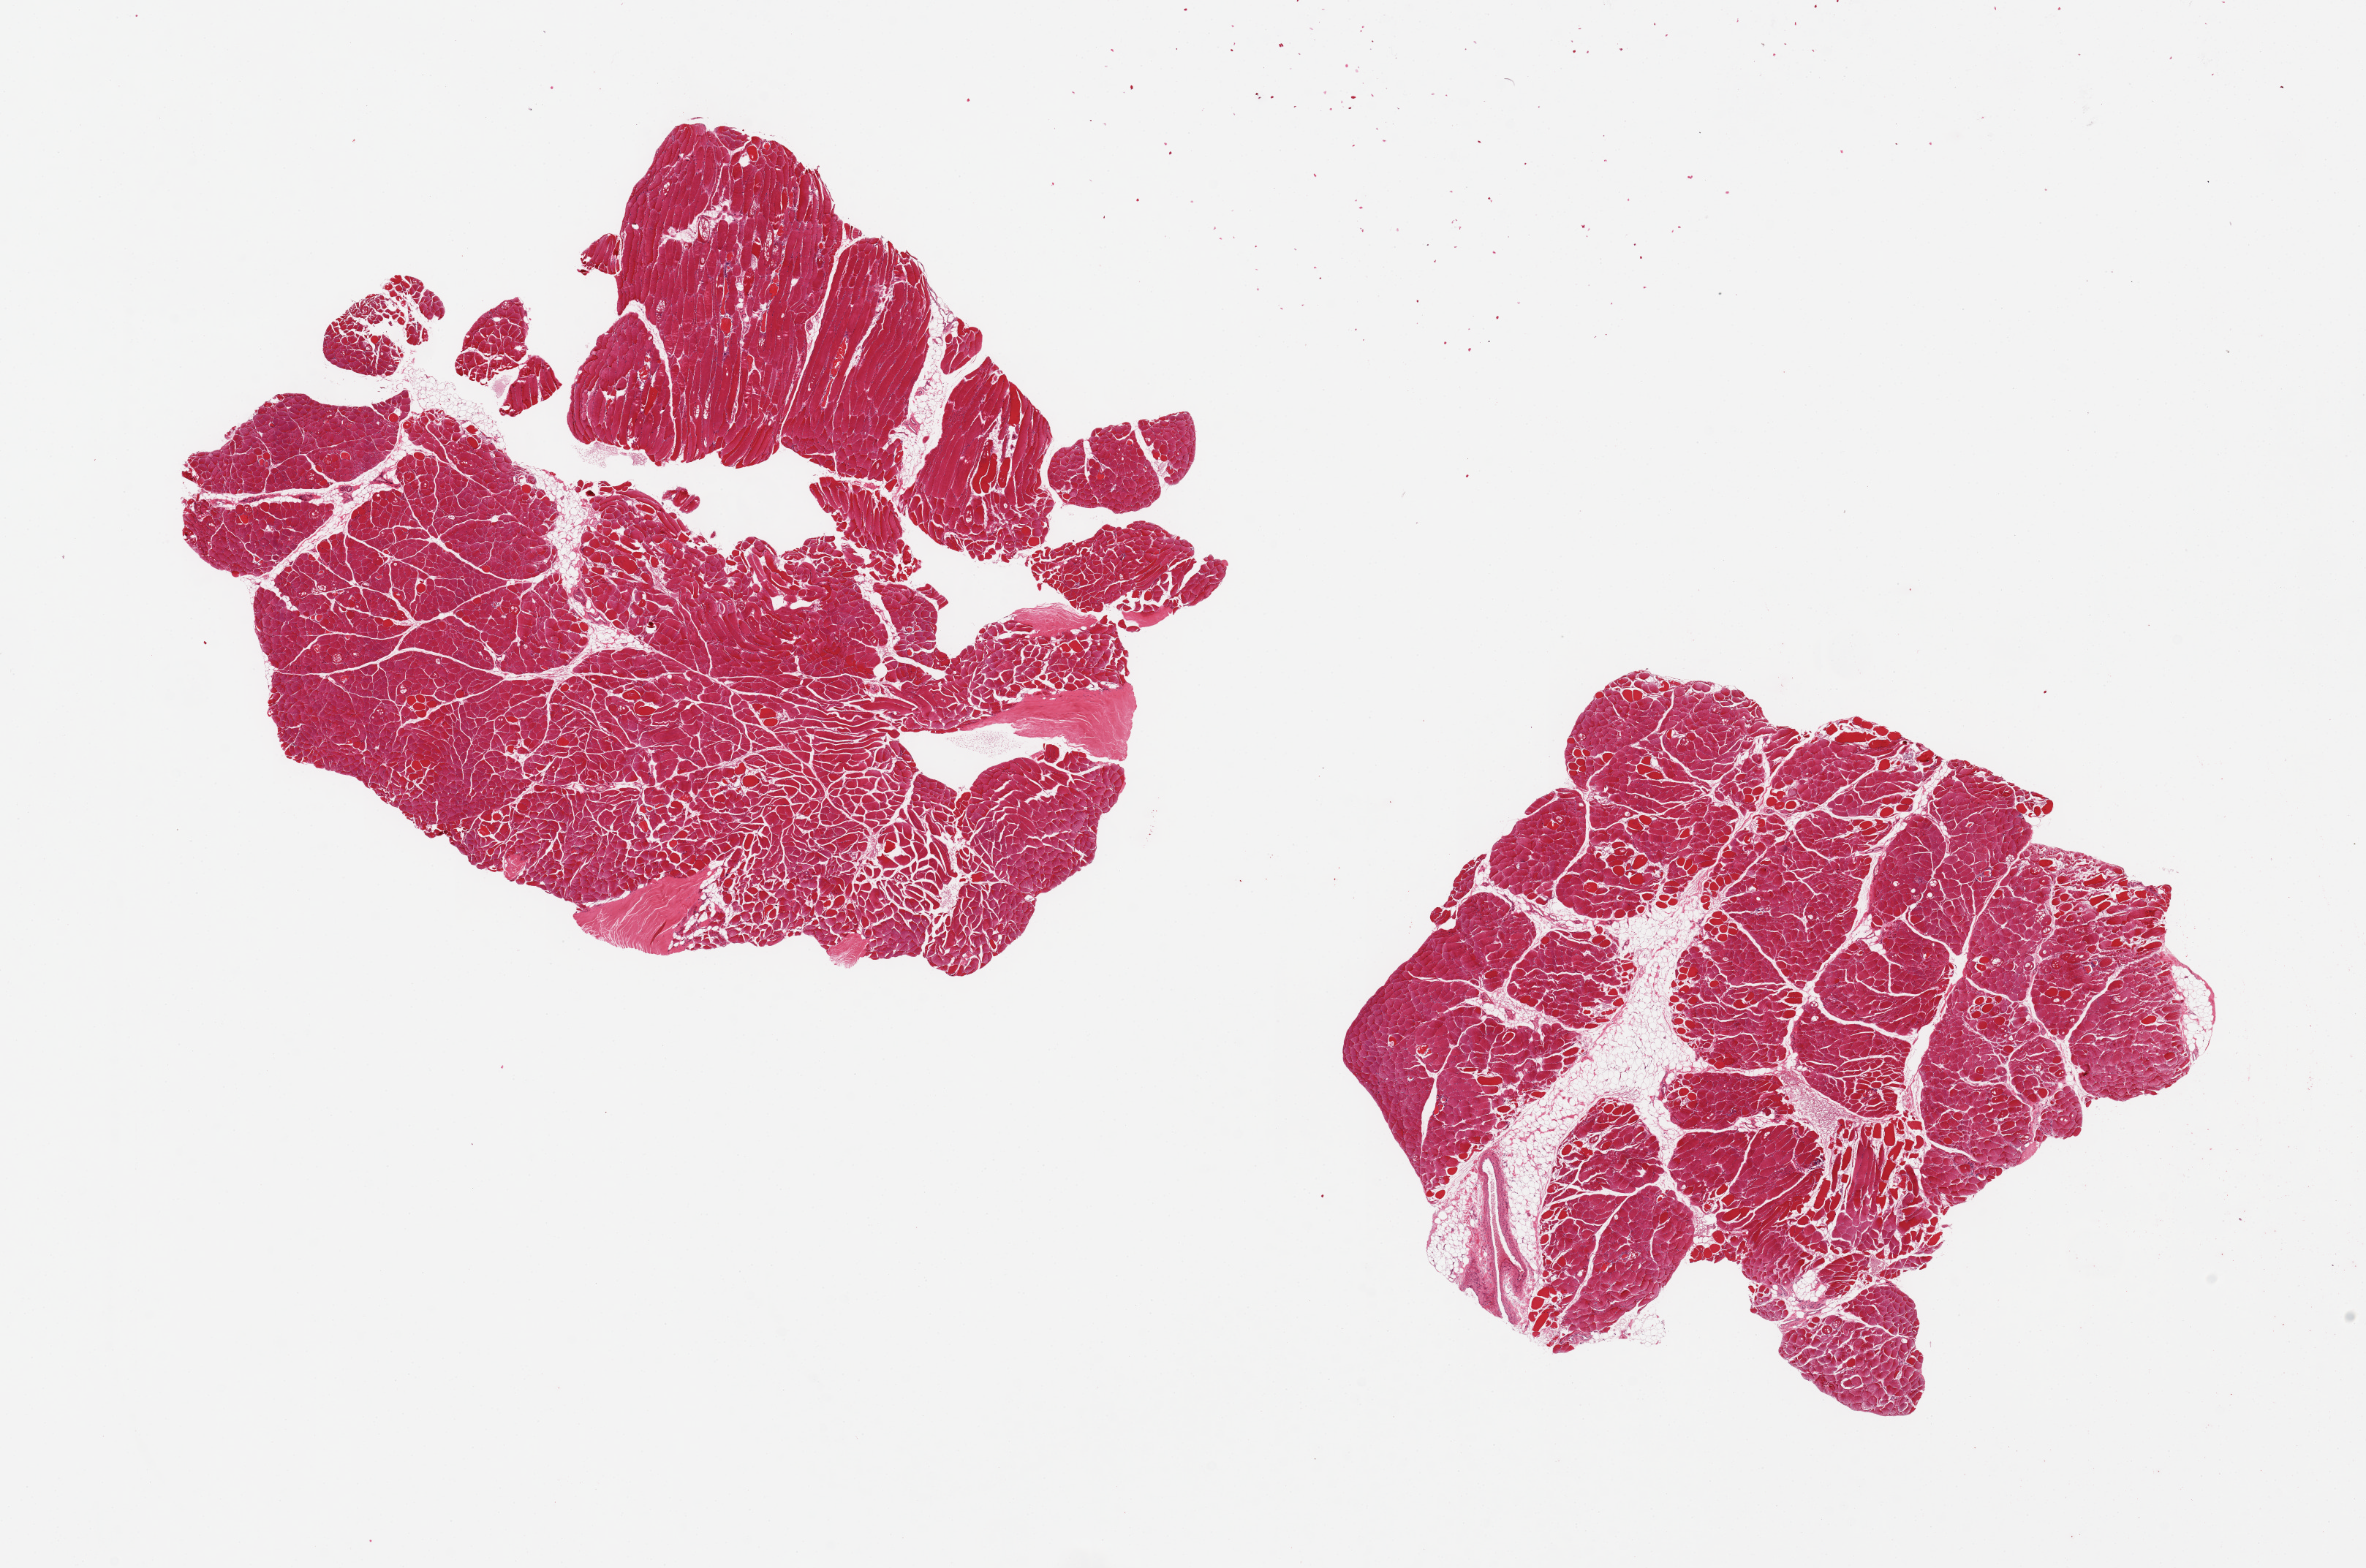
Whole-slide image, H&E stain — shown as a low-resolution overview of the whole scanned area (about 25.6 x 17.0 mm, from a 20x scan), PAXgene-fixed, paraffin-embedded tissue, sampled site (target tissue): skeletal muscle, tissue donor sample. Donor sex: male.
Reviewer comment on this tissue sample: 2 pieces. 10% internal adipose.